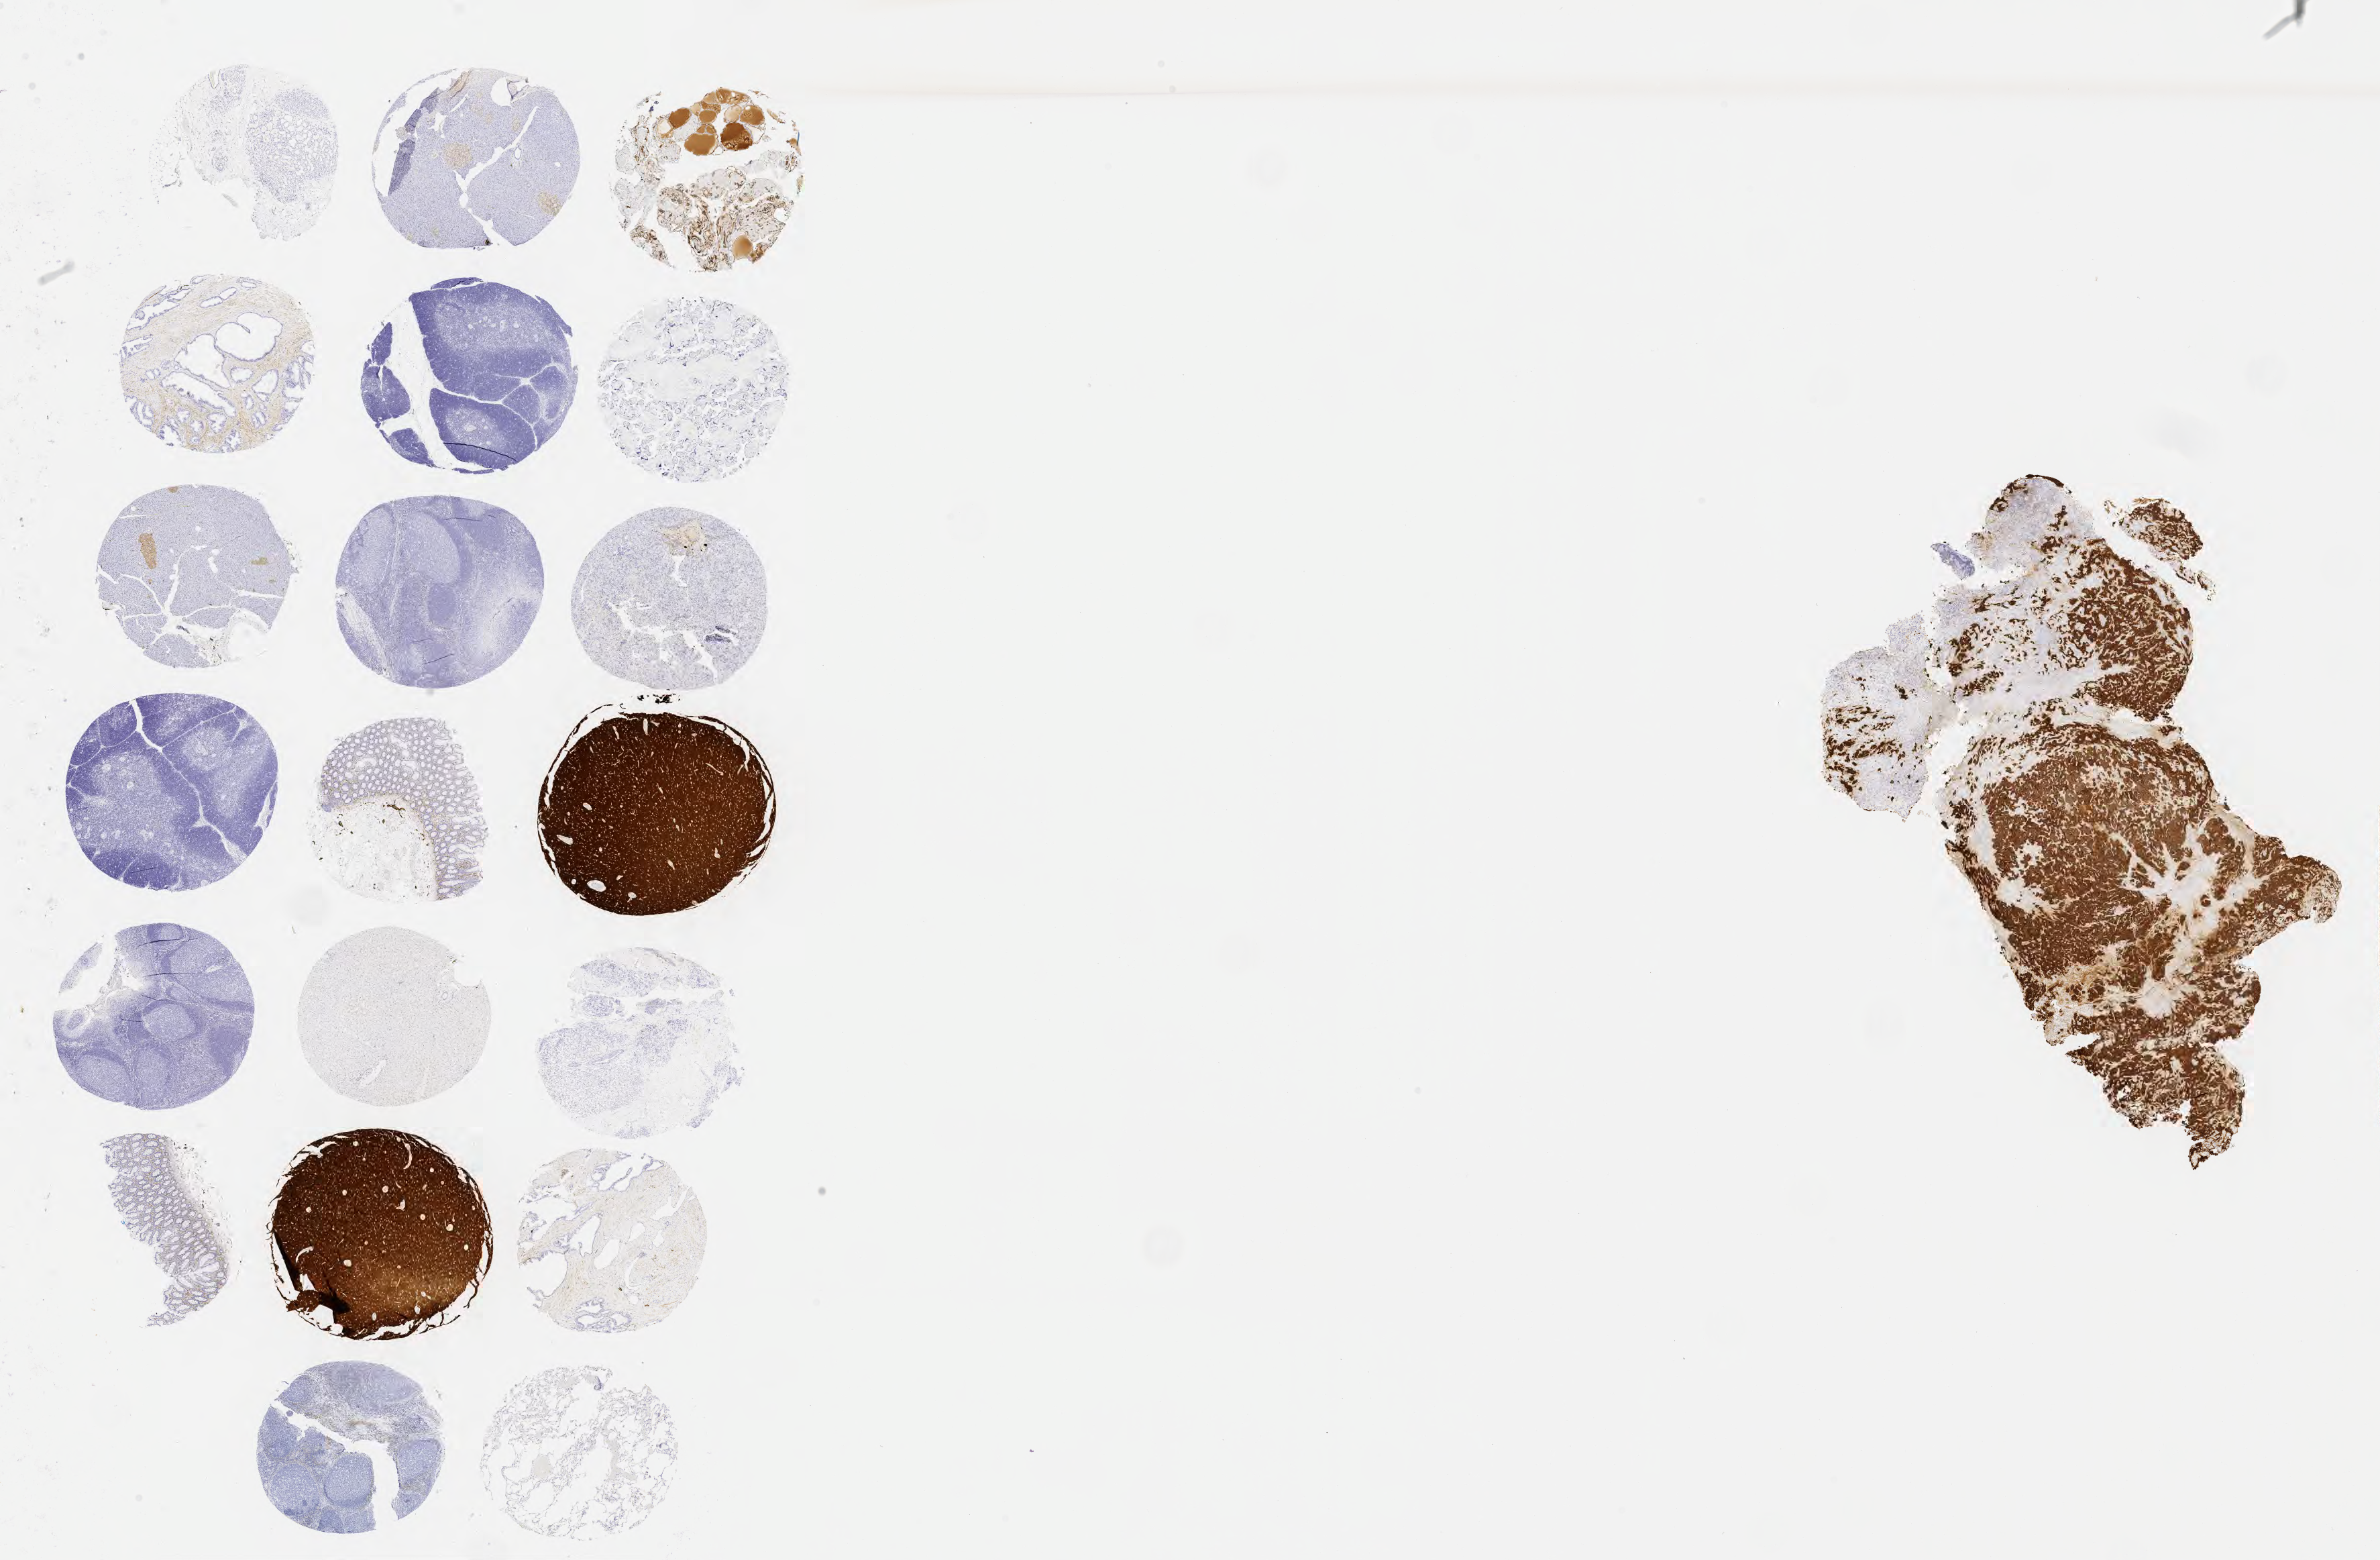
Immunohistochemistry (IHC) whole-slide image stained for CD56, low-resolution overview of the scanned area, about 28.7 x 18.8 mm. Specimen: tumor tissue. Site: cervix. Patient female; age 43 years.
• diagnosis: Lymphoepithelial carcinoma